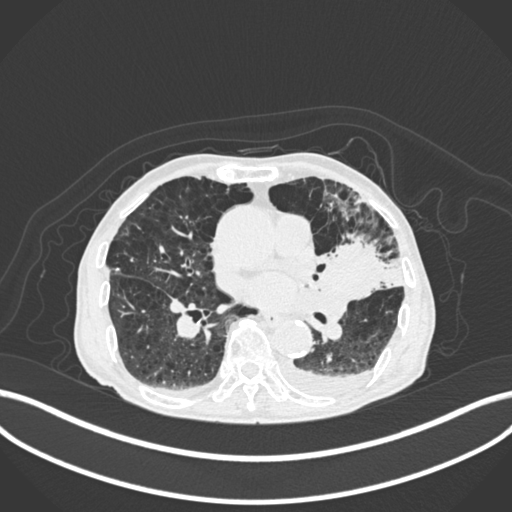
Chest CT, one axial slice; position 102 of 400 along the scan axis; reconstruction kernel B30f; lung window (W 1500 / L -600 HU); 1 mm slice thickness; 512 × 512 image matrix, field of view 400 × 400 mm. Male patient, age 90 years or older. Case-level facts recorded for this patient, not image findings: clinical TNM (as recorded): T2b N1 M0.
Outlined on this slice (bounding box drawn by a radiologist):
- lung tumour (recorded histology: squamous cell carcinoma): bounding box <315,235,388,307> (left, top, right, bottom; pixels)